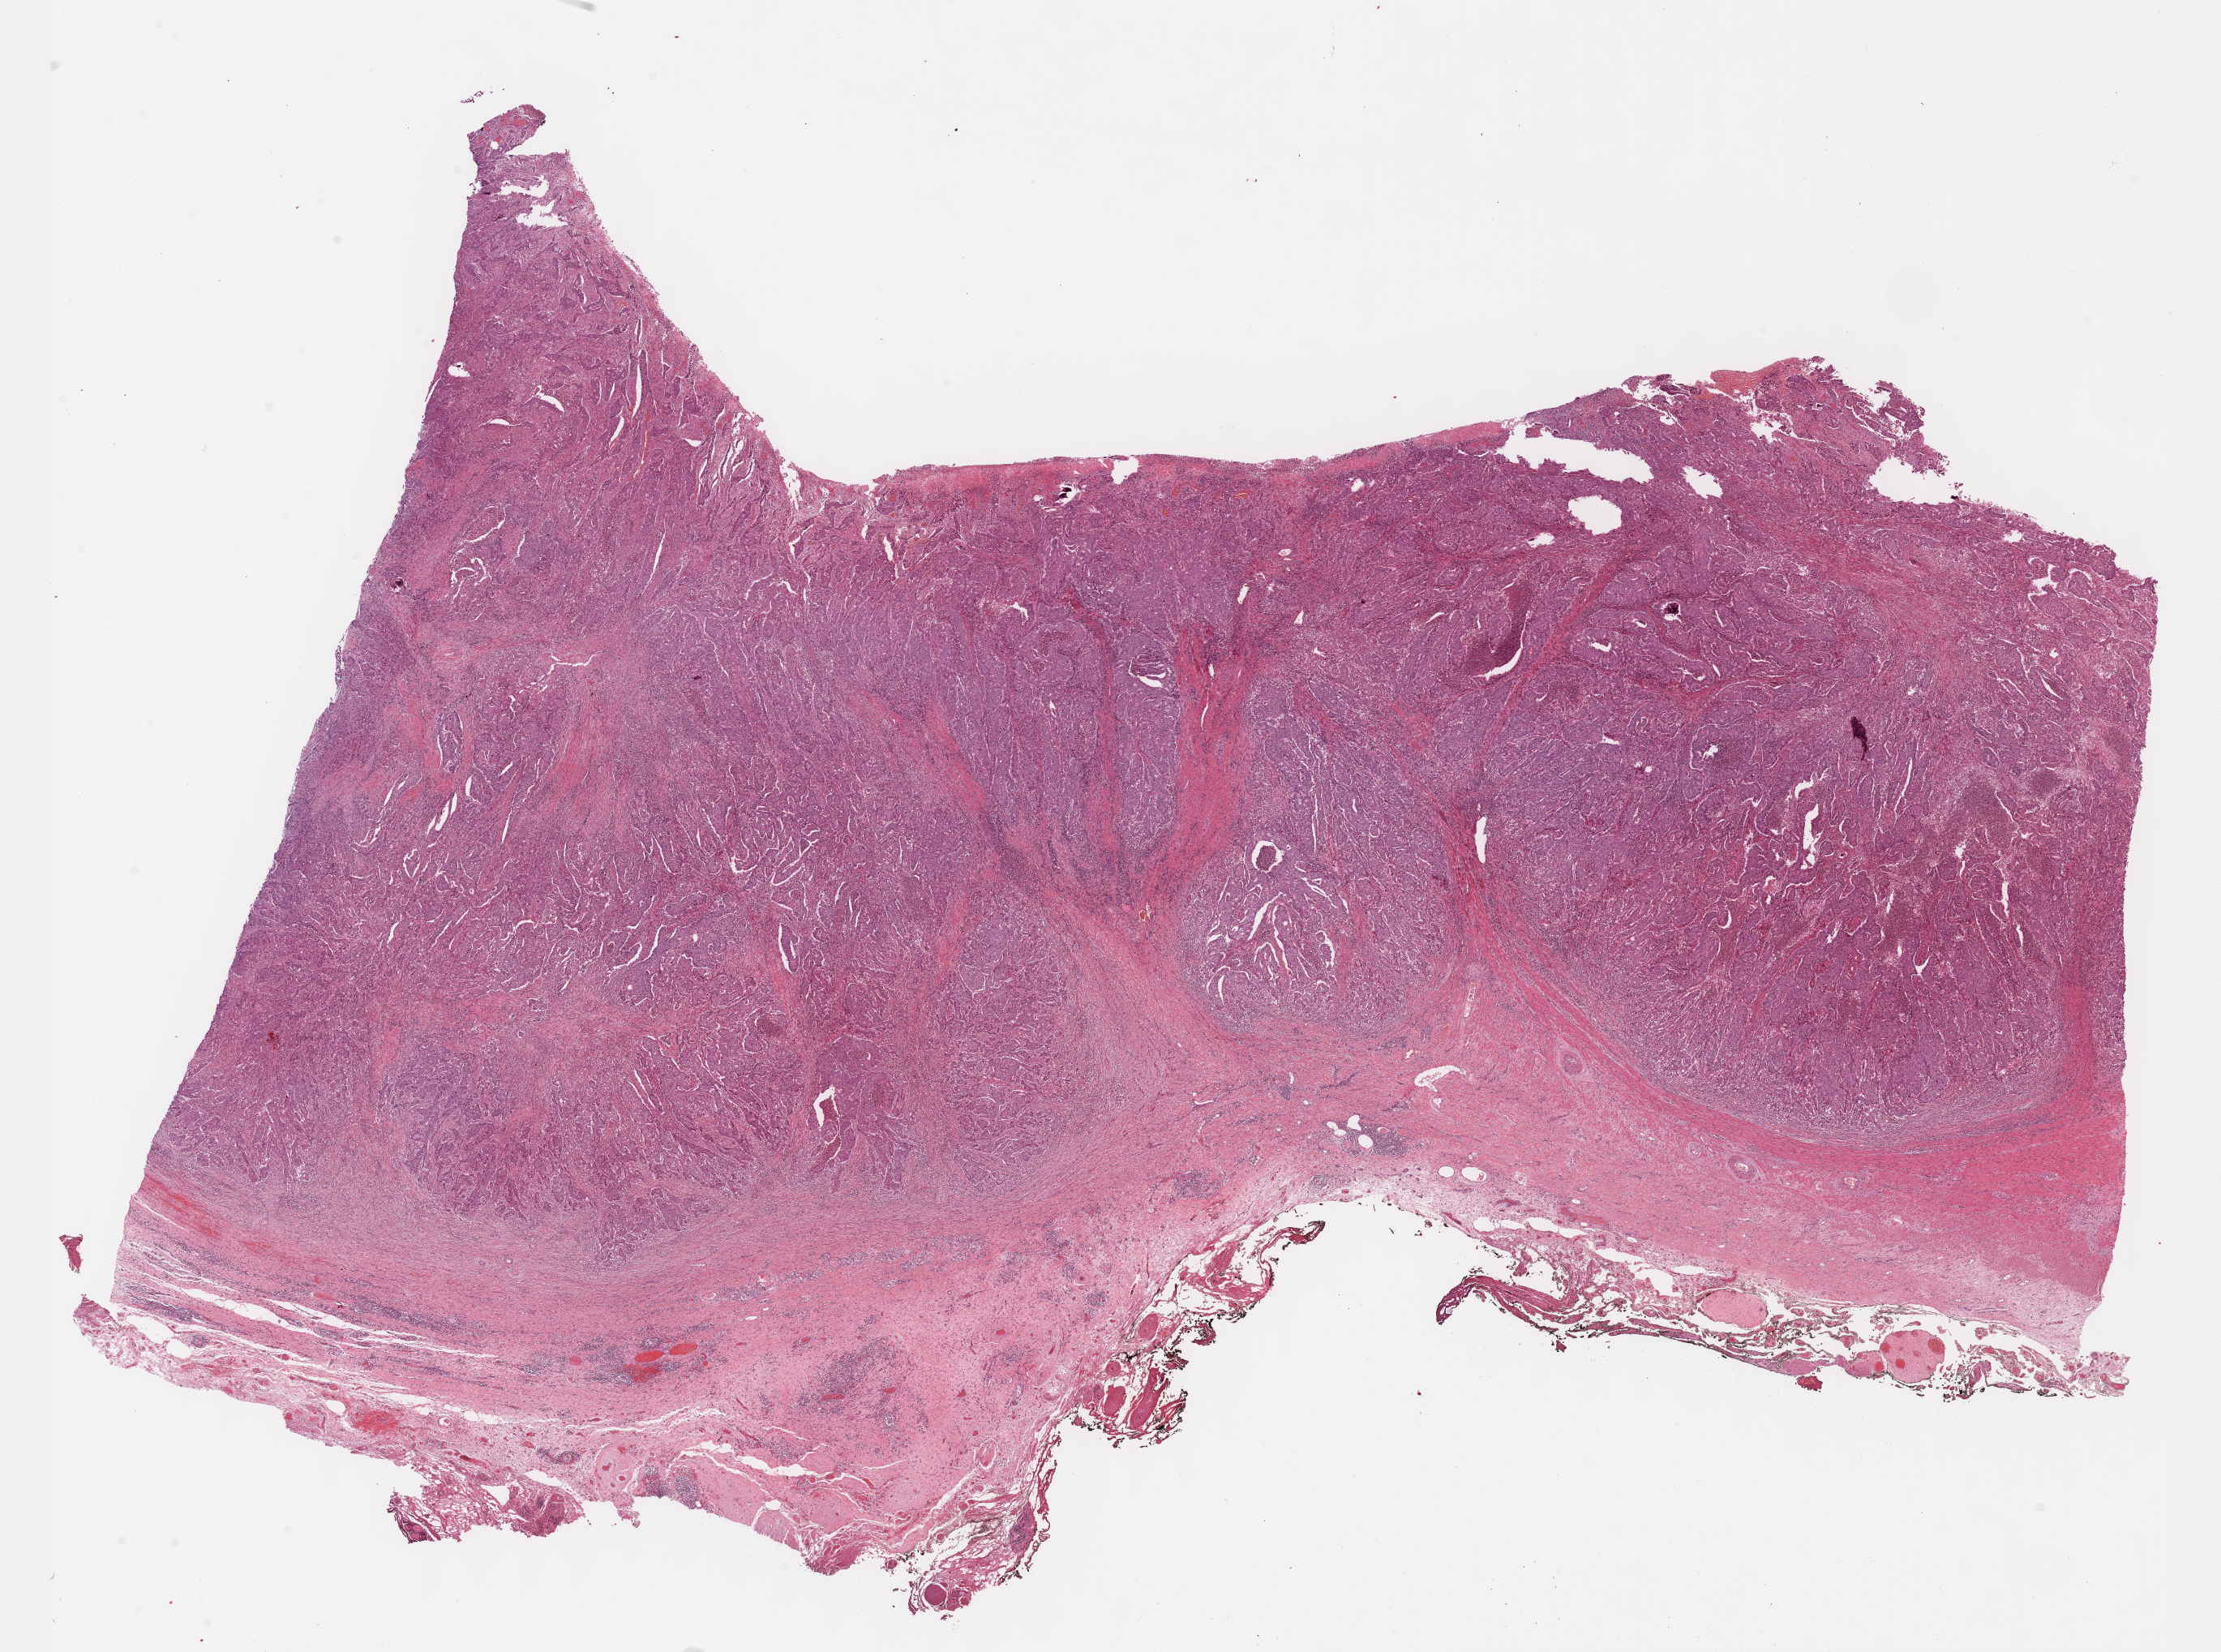
Digitized H&E-stained tissue section (whole slide), shown as a low-resolution overview of the whole scanned area (about 22.1 x 16.5 mm, acquisition: 40x scan). Formalin-fixed paraffin-embedded (FFPE) diagnostic section. Stomach, primary tumour sample. Patient: male, age at initial diagnosis 67 years. Histologic grade: G3 (poorly differentiated).
Pathologic diagnosis: Adenocarcinoma, intestinal type (body of stomach). AJCC pathologic stage: IIA (7th edition). TNM: T3 N0 M0.